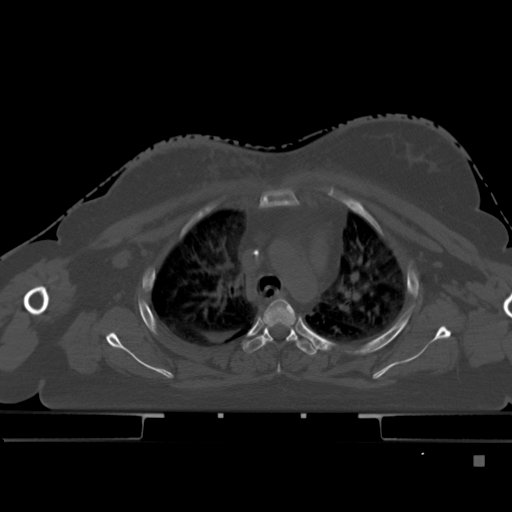
CT including the spine, one axial slice; position 338 of 495 along the scan axis; bone window (W 1800 / L 400 HU); 1.5 mm slice thickness; 512 × 512 image matrix, field of view 404 × 404 mm. Patient: female, 33 years. From the clinical record (not read from this slice): primary cancer: breast.
Outlined on this slice (semi-automatically segmented with operator editing):
- T3 vertebra: bounding box [x1, y1, x2, y2] px = [261, 297, 295, 343]
- T4 vertebra: [243, 321, 320, 355]